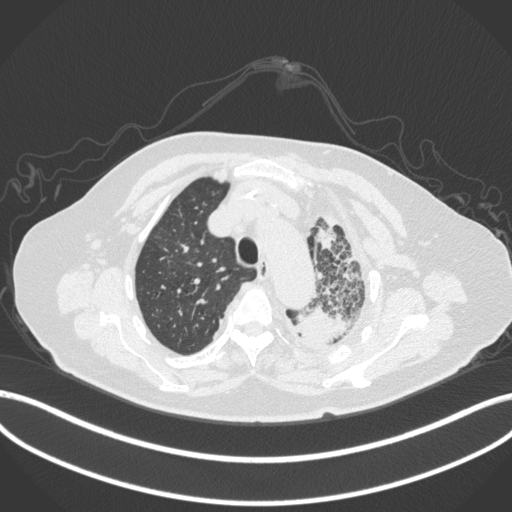
Chest CT, one axial slice; position 309 of 399 along the scan axis; reconstruction kernel B31f; lung window (W 1500 / L -600 HU); 1 mm slice thickness; 512 × 512 image matrix. Female patient, age 75 years. Case-level facts recorded for this patient, not image findings: clinical TNM (as recorded): T3 N3 M1.
Outlined on this slice (rectangle marked by the reading radiologist):
- lung tumour (recorded histology: adenocarcinoma): bounding box [x1, y1, x2, y2] px = [291, 300, 363, 351]